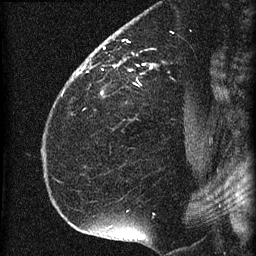
Breast MRI (dynamic contrast-enhanced), one sagittal slice. Slice 46 of 60 in the series (ordered by position). Dynamic contrast-enhanced series, image 2 of 4 at this slice position (ordered by acquisition). 1.5 T. TE 4.2 ms, TR 22.7 ms. 1.5 mm slice thickness. 256 × 256 image matrix, field of view 180 × 180 mm. Patient: female, 35 years. From the clinical record (not read from this slice): setting: breast cancer imaged before/during neoadjuvant chemotherapy; receptor status: HR-positive, HER2-negative.
Outlined on this slice (semi-automatic segmentation, software-assisted and operator-edited):
- analysis volume of interest (the breast-tissue region the enhancement analysis was run in; not a lesion): bounding box [x1, y1, x2, y2] px = [69, 27, 199, 112]
- tumour enhancement mask (voxels above the 90 % enhancement threshold inside the analysis volume of interest): [76, 39, 155, 76]